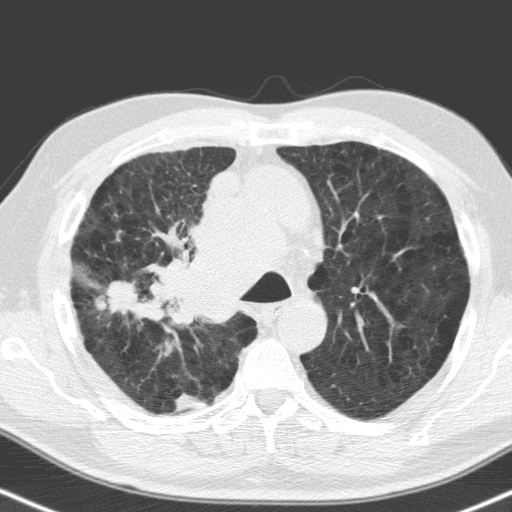
Axial slice from a low-dose chest CT screening exam, baseline screening round, lung window (W 1500 / L -600 HU), 3.2 mm slice thickness, standard (soft-tissue) reconstruction kernel (C), 120 kVp, slice 46 of 160 in the series, 512 × 512 image matrix, field of view 324 × 324 mm. Male, age 71 years at enrolment. Former smoker at enrolment.
• Expert reader's lesion annotation, bounding box <92,272,169,337> (left, top, right, bottom; pixels).
• The screening reader recorded 2 non-calcified nodules or masses ≥4 mm on this exam; which of them this box marks is not recorded.
• Later outcome: lung cancer diagnosed 31 days after this screen — small cell carcinoma, NOS, right upper lobe, stage IV (AJCC 6th edition), 40 mm at pathology.